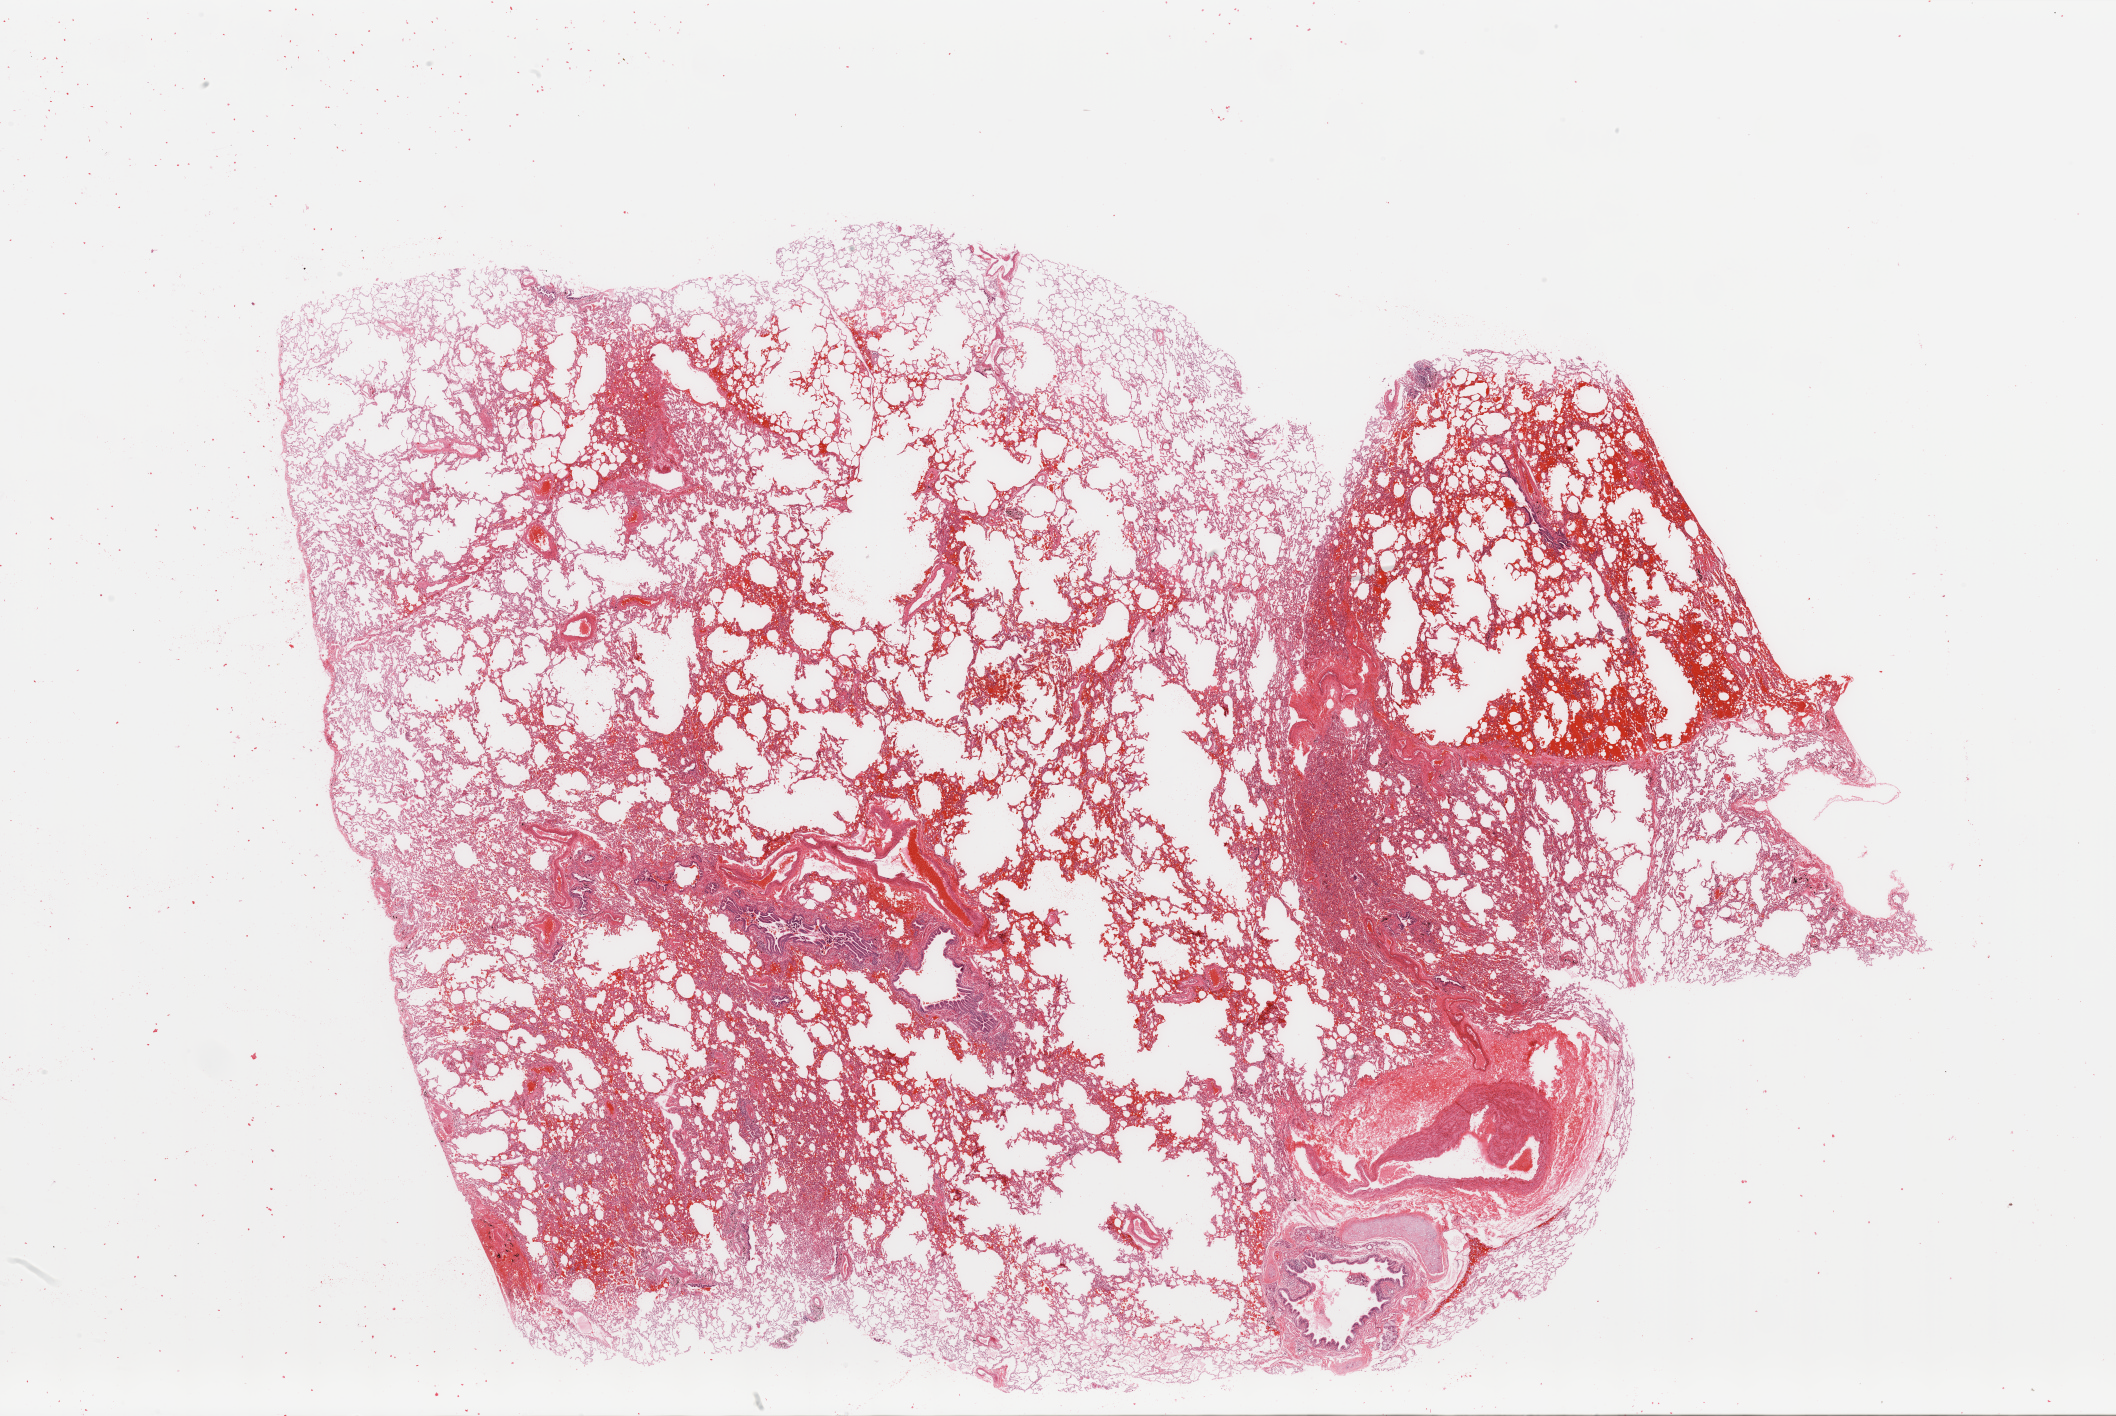
Digitized Hematoxylin and eosin (H&E) stained tissue section (whole slide) — low-resolution overview of the scanned area, about 33.5 x 22.4 mm (acquisition: 20x scan); normal (non-tumour) tissue sample, sampled site: lung. Male, 55 y/o.
* this section: normal (non-tumour) tissue from the same patient
* patient diagnosis: Adenocarcinoma, NOS